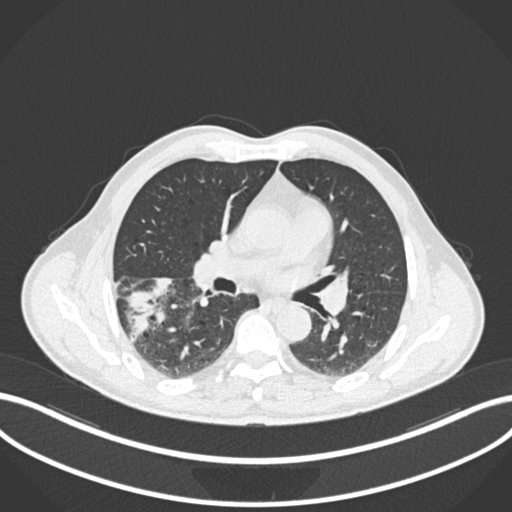
Chest CT, one axial slice; reconstruction kernel B30f; 120 kVp; lung window (W 1500 / L -600 HU); 512 × 512 image matrix, field of view 400 × 400 mm. Patient: male, 58 years. From the clinical record (not read from this slice): clinical TNM (as recorded): T3 N0 M0; histopathological grade: G2.
Annotated regions visible in this slice (rectangle marked by the reading radiologist):
- lung tumour (recorded histology: squamous cell carcinoma): bounding box (x1, y1, x2, y2) in pixels: (123, 270, 173, 346)